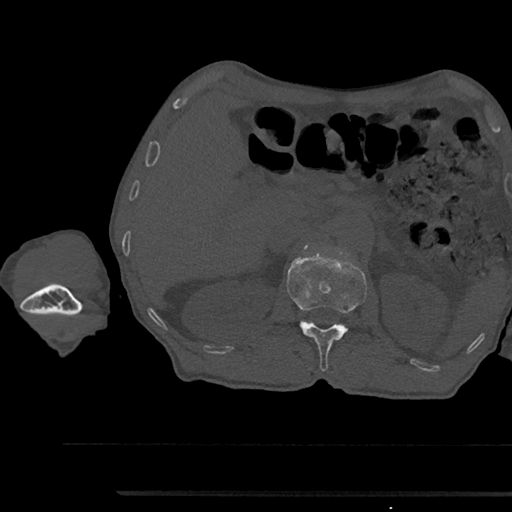
CT including the spine, one axial slice. Bone window (W 1800 / L 400 HU). 512 × 512 image matrix, field of view 367 × 367 mm. Male patient, age 79 years. Case-level facts recorded for this patient, not image findings: primary cancer: prostate.
Annotated regions visible in this slice (semi-automatically segmented with operator editing):
- L1 vertebra: bounding box [x1, y1, x2, y2] px = [286, 246, 367, 371]